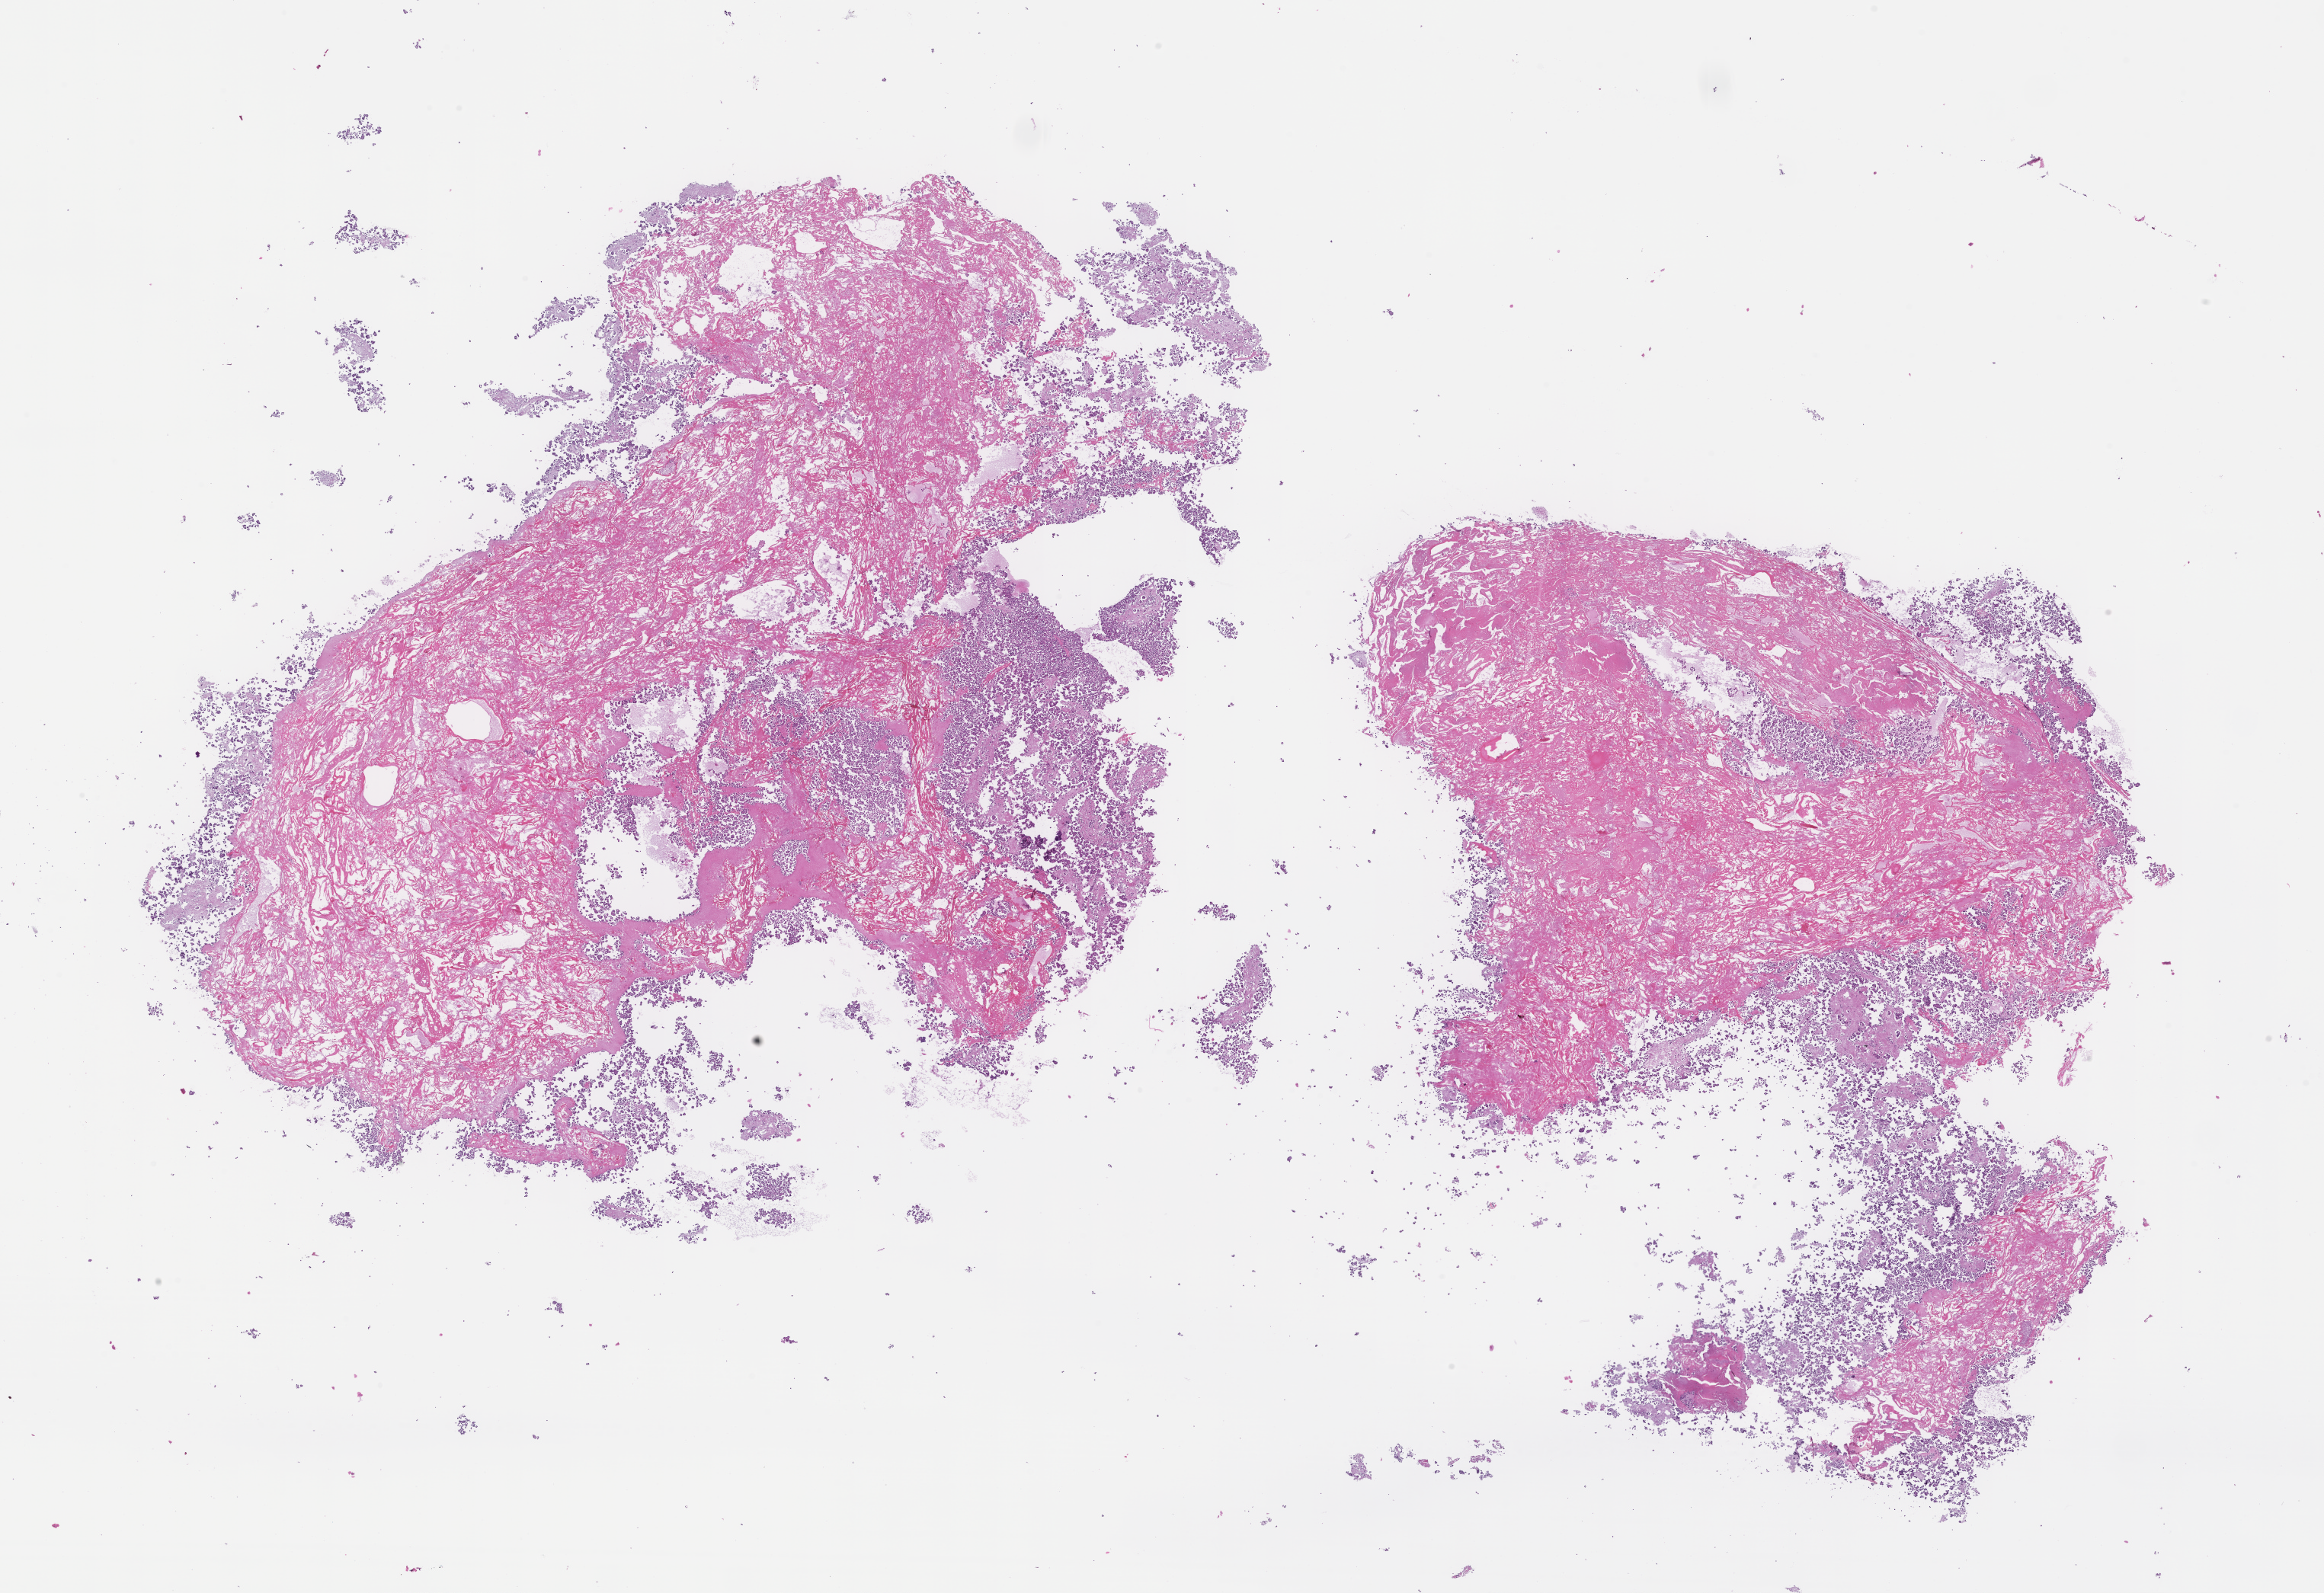
Hematoxylin and eosin (H&E) whole-slide image, whole scanned area (about 24.6 x 16.9 mm) shown as a low-resolution overview; formalin-fixed, paraffin-embedded (FFPE) tissue; tissue site: lung; specimen time point: archival tissue. Patient sex: male.
This section: primary tumor. Diagnosis: Non-Small Cell Lung Carcinoma.